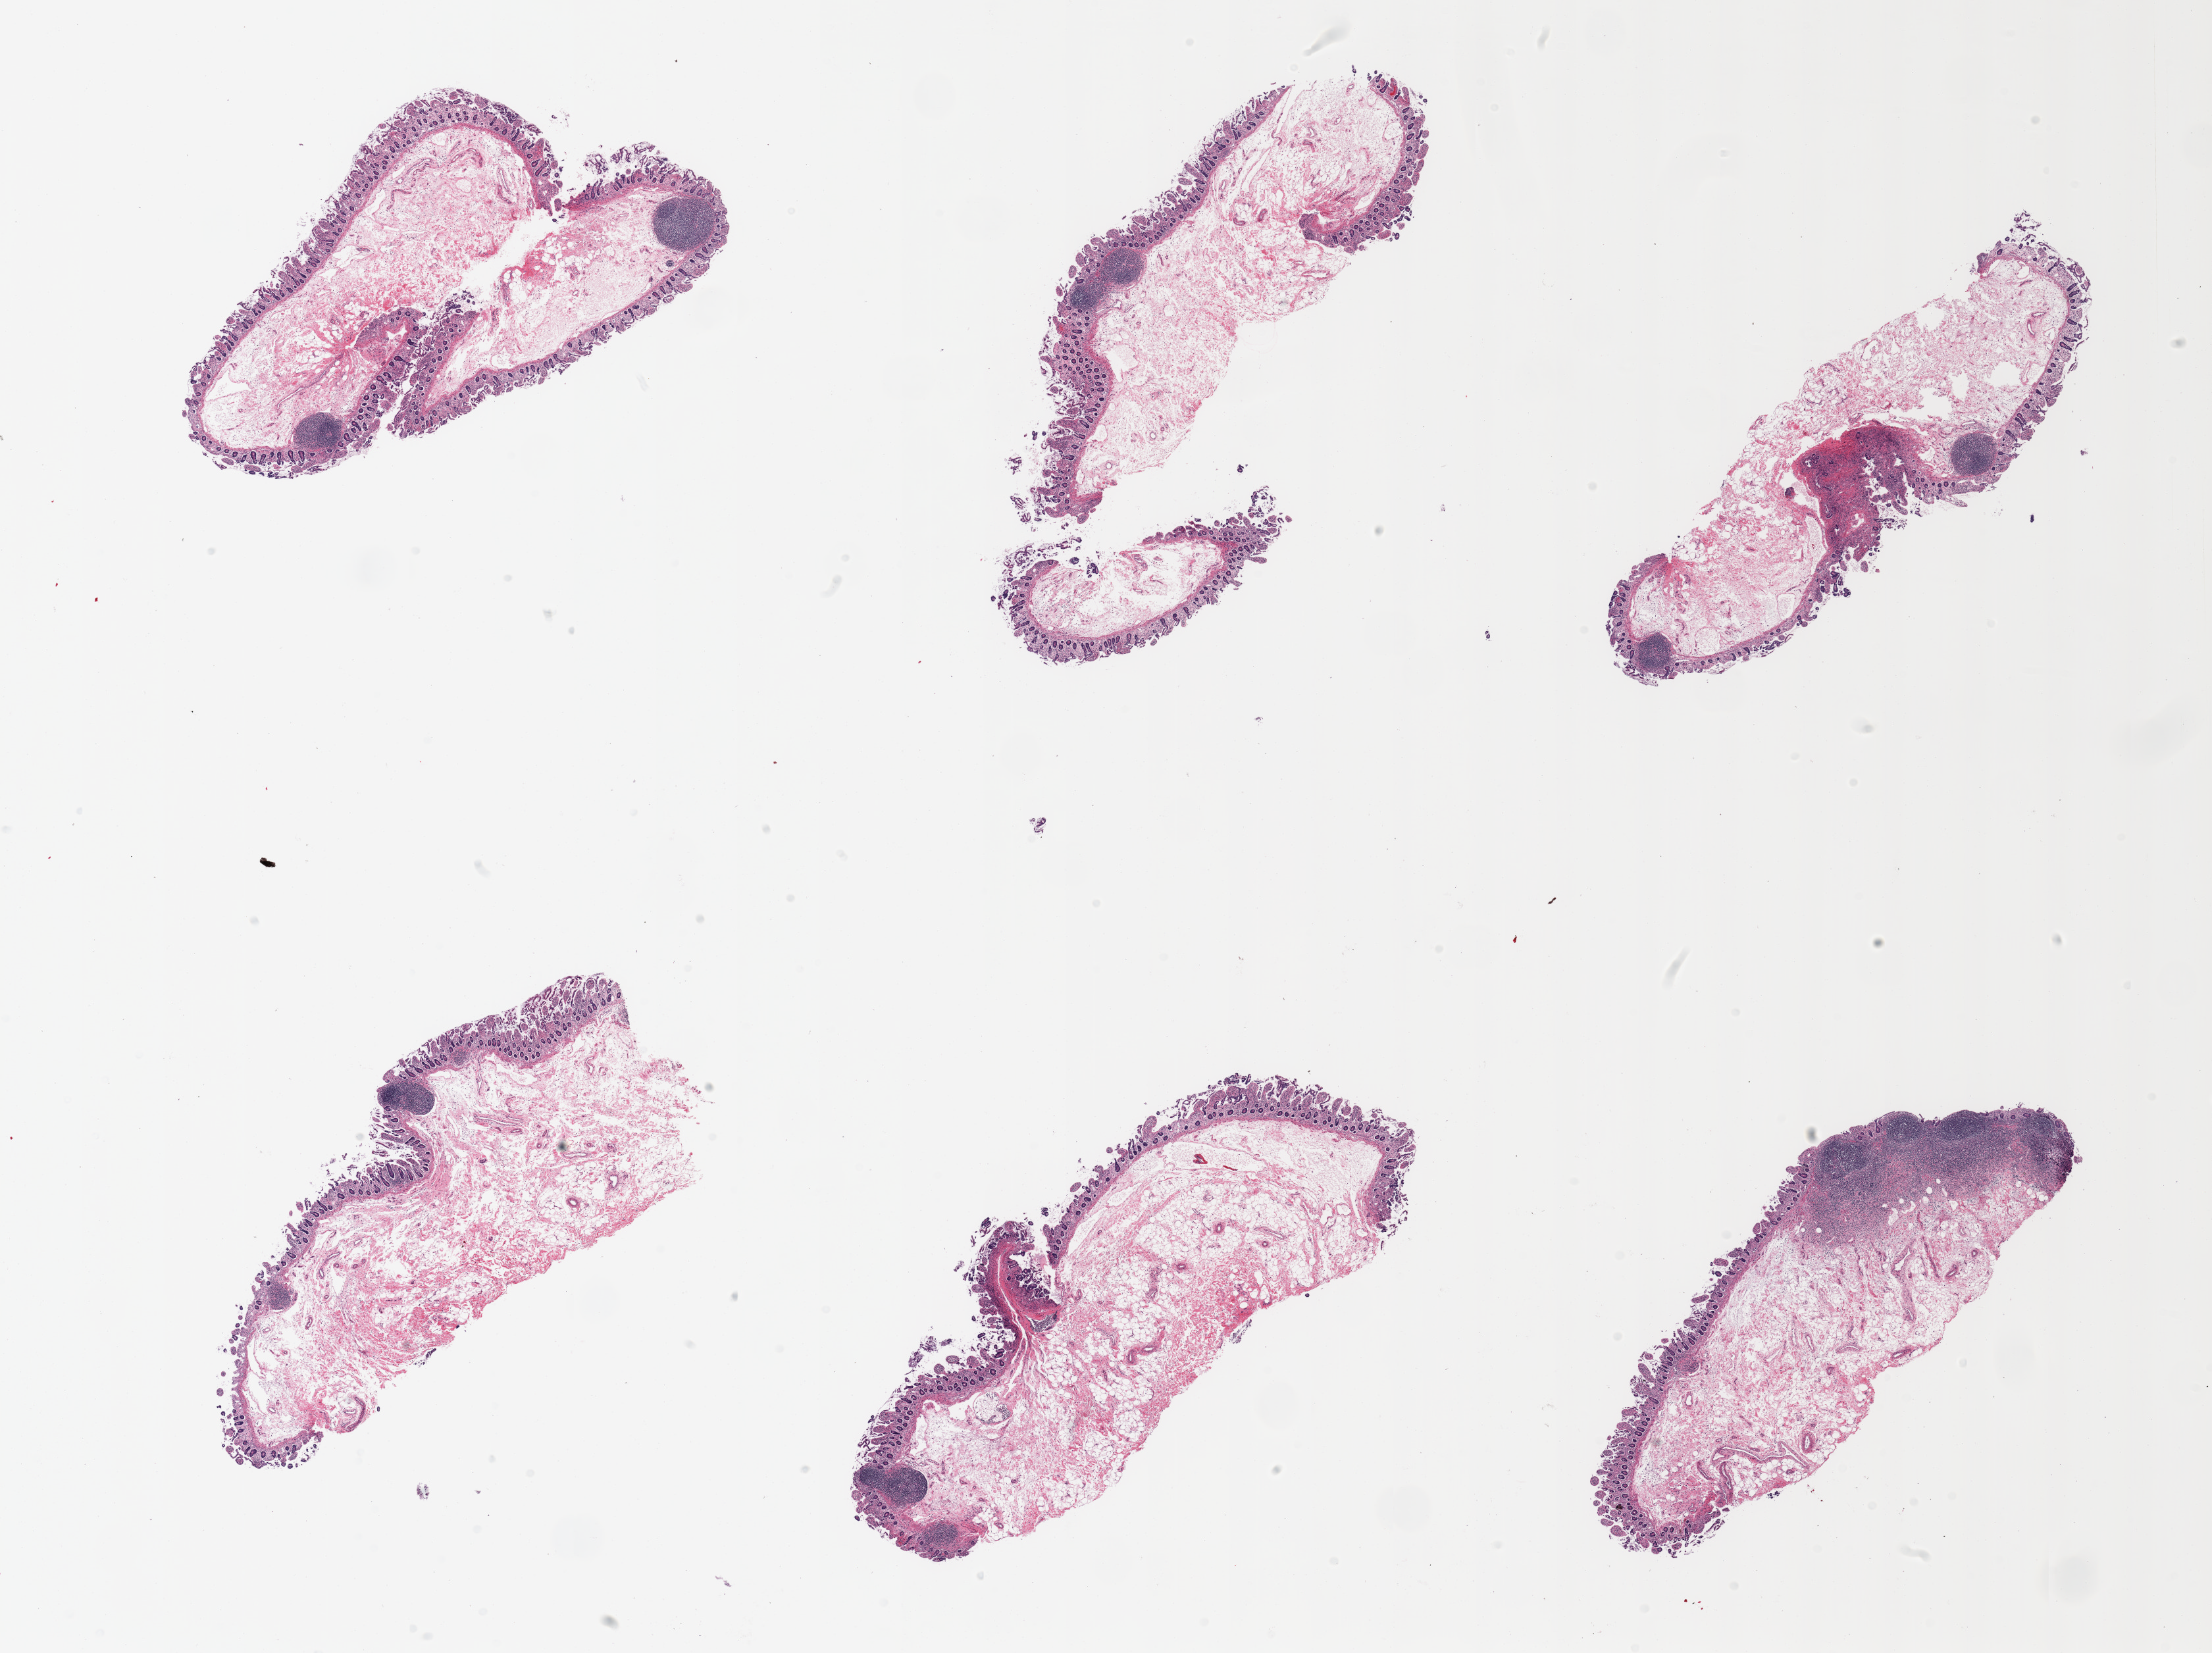
Digitized hematoxylin and eosin (H&E)-stained section — low-resolution overview of the scanned area, about 26.6 x 19.9 mm; PAXgene-fixed, paraffin-embedded tissue; sampled site (target tissue): ileum; donor tissue sample. Donor sex: male.
* reviewer comment on this tissue sample: 6 pieces; moderately to severly autolyzed mucosa; residual target lymphoid aggregates are ~15 % of tissue